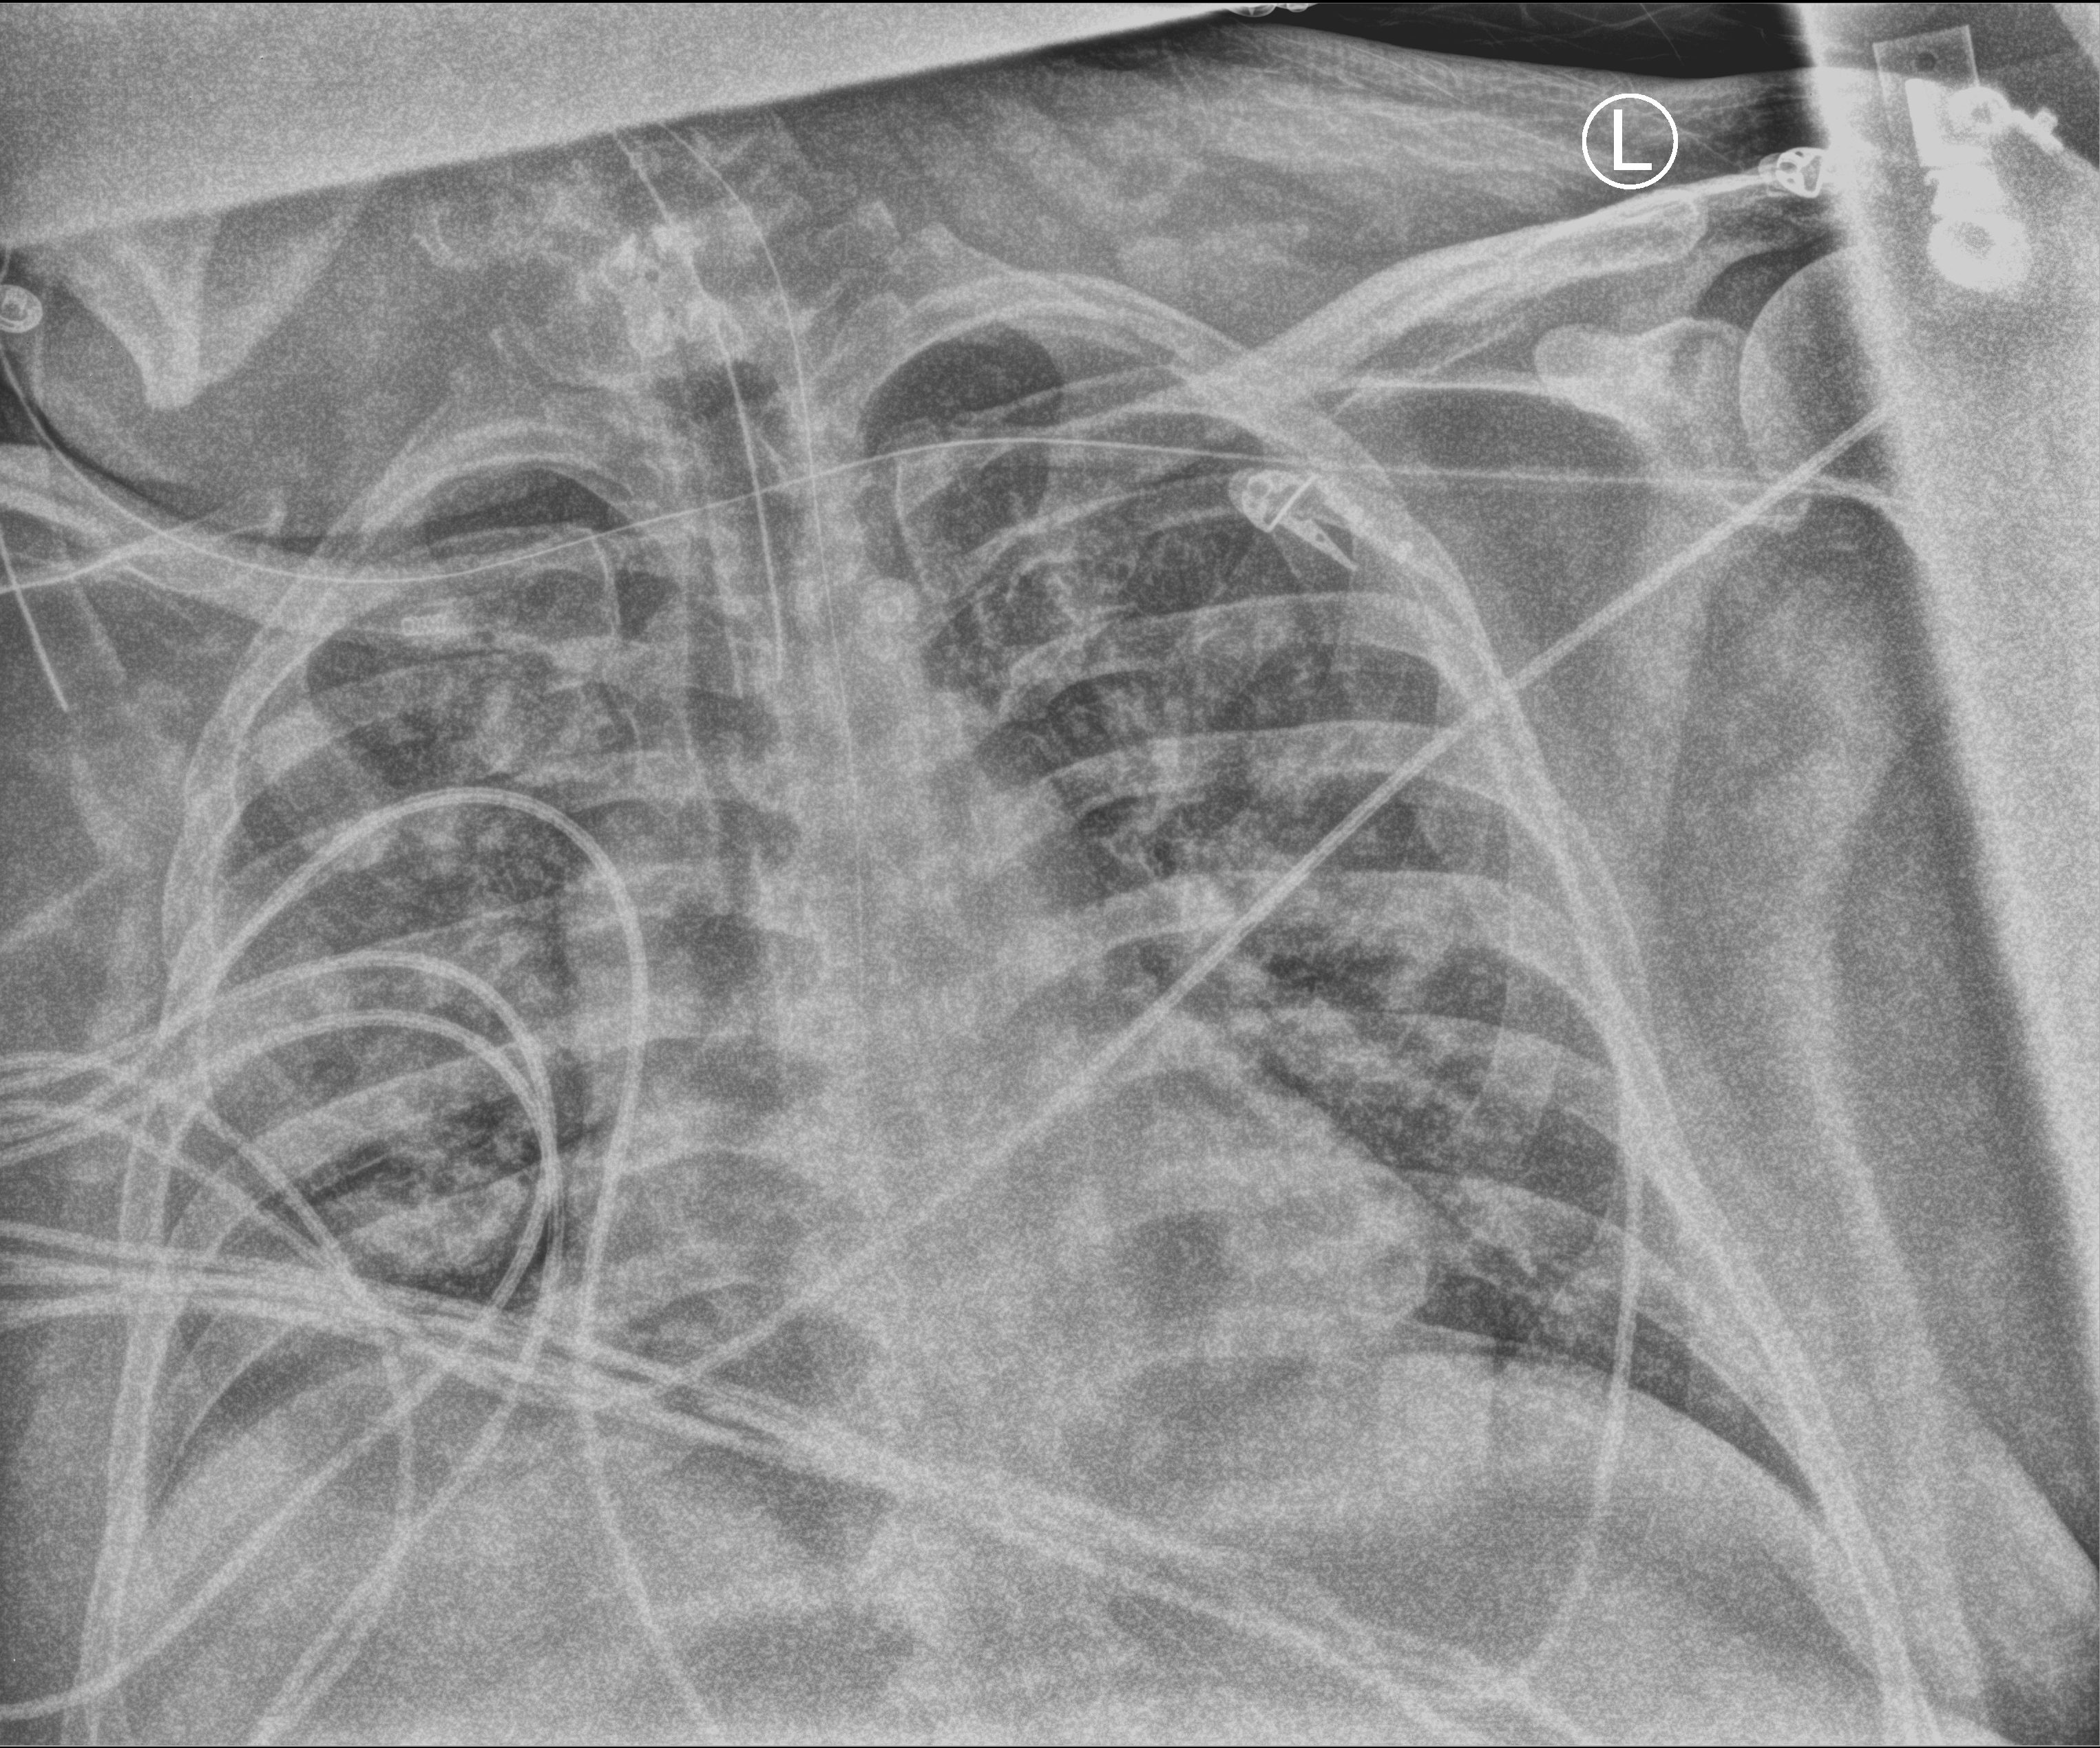
Portable chest radiograph. Male patient hospitalised with COVID-19, age 18–59 years.
Admission-level facts for this patient (not findings on this image; timing relative to this image not recorded): mechanically ventilated during this hospital stay: yes; admitted to intensive care during this hospital stay: yes.